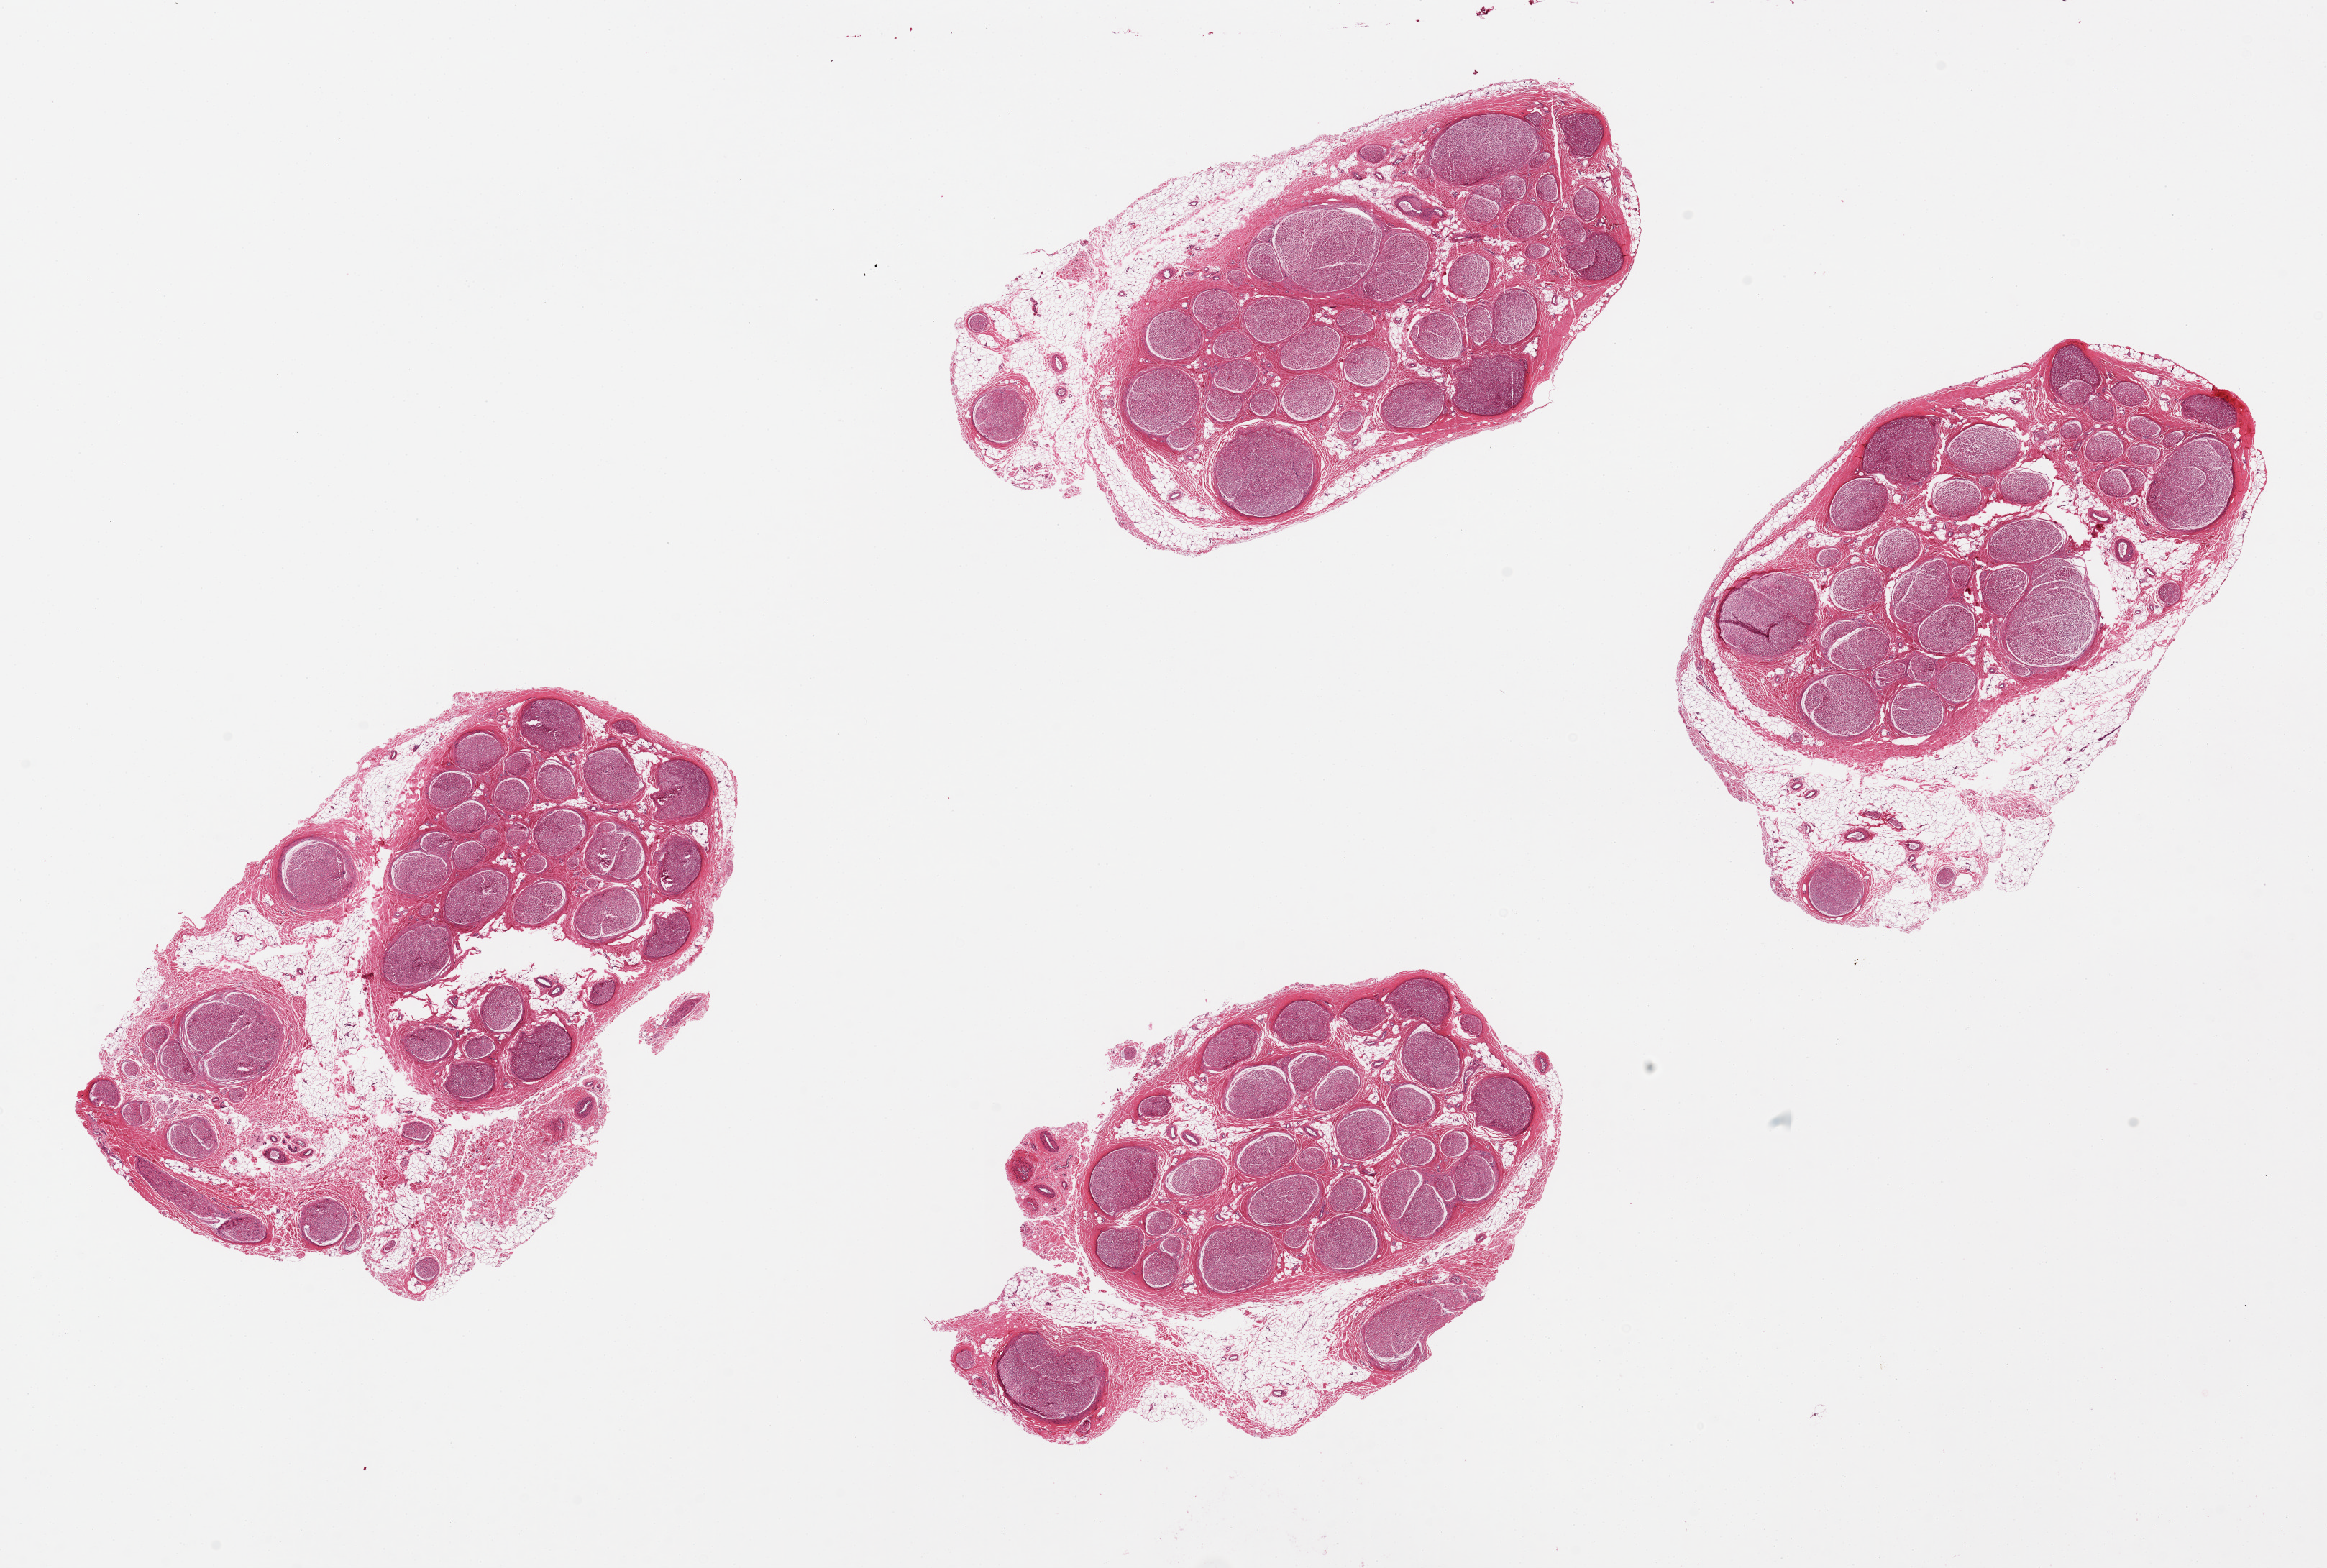
Whole-slide image, hematoxylin and eosin (H&E) stain, brightfield, shown as a low-resolution overview of the whole scanned area (about 25.6 x 17.3 mm, slide scanned at 20x). PAXgene-fixed, paraffin-embedded tissue. Section of tibial nerve (target tissue). Donor tissue sample. Donor: male.
Reviewer comment on this tissue sample: 4 pieces, up to 8x5mm; Each with 30% adipose.